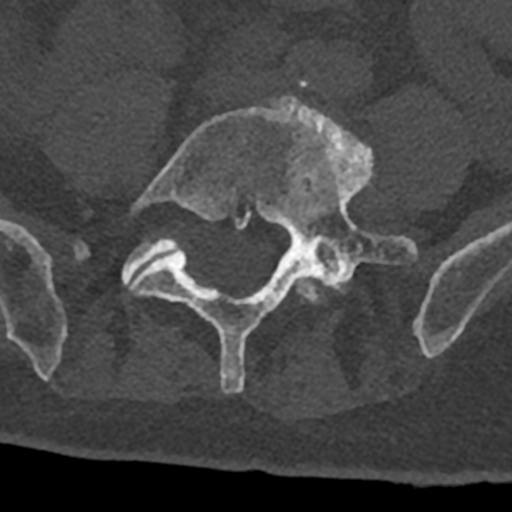
CT including the spine, one axial slice. Position 202 of 797 along the scan axis. 120 kVp. Bone window (W 1800 / L 400 HU). 512 × 512 image matrix, field of view 160 × 160 mm. Patient: male, 74 years. Case-level facts recorded for this patient, not image findings: primary cancer: renal; vertebrae with lytic lesions (as recorded): T10, L1, L2, L3, L4, L5.
Annotated regions visible in this slice (semi-automatically segmented with operator editing):
- L4 vertebra: box from (x=290, y=276) to (x=320, y=303) px
- L5 vertebra: (x=130, y=96)–(x=418, y=393)